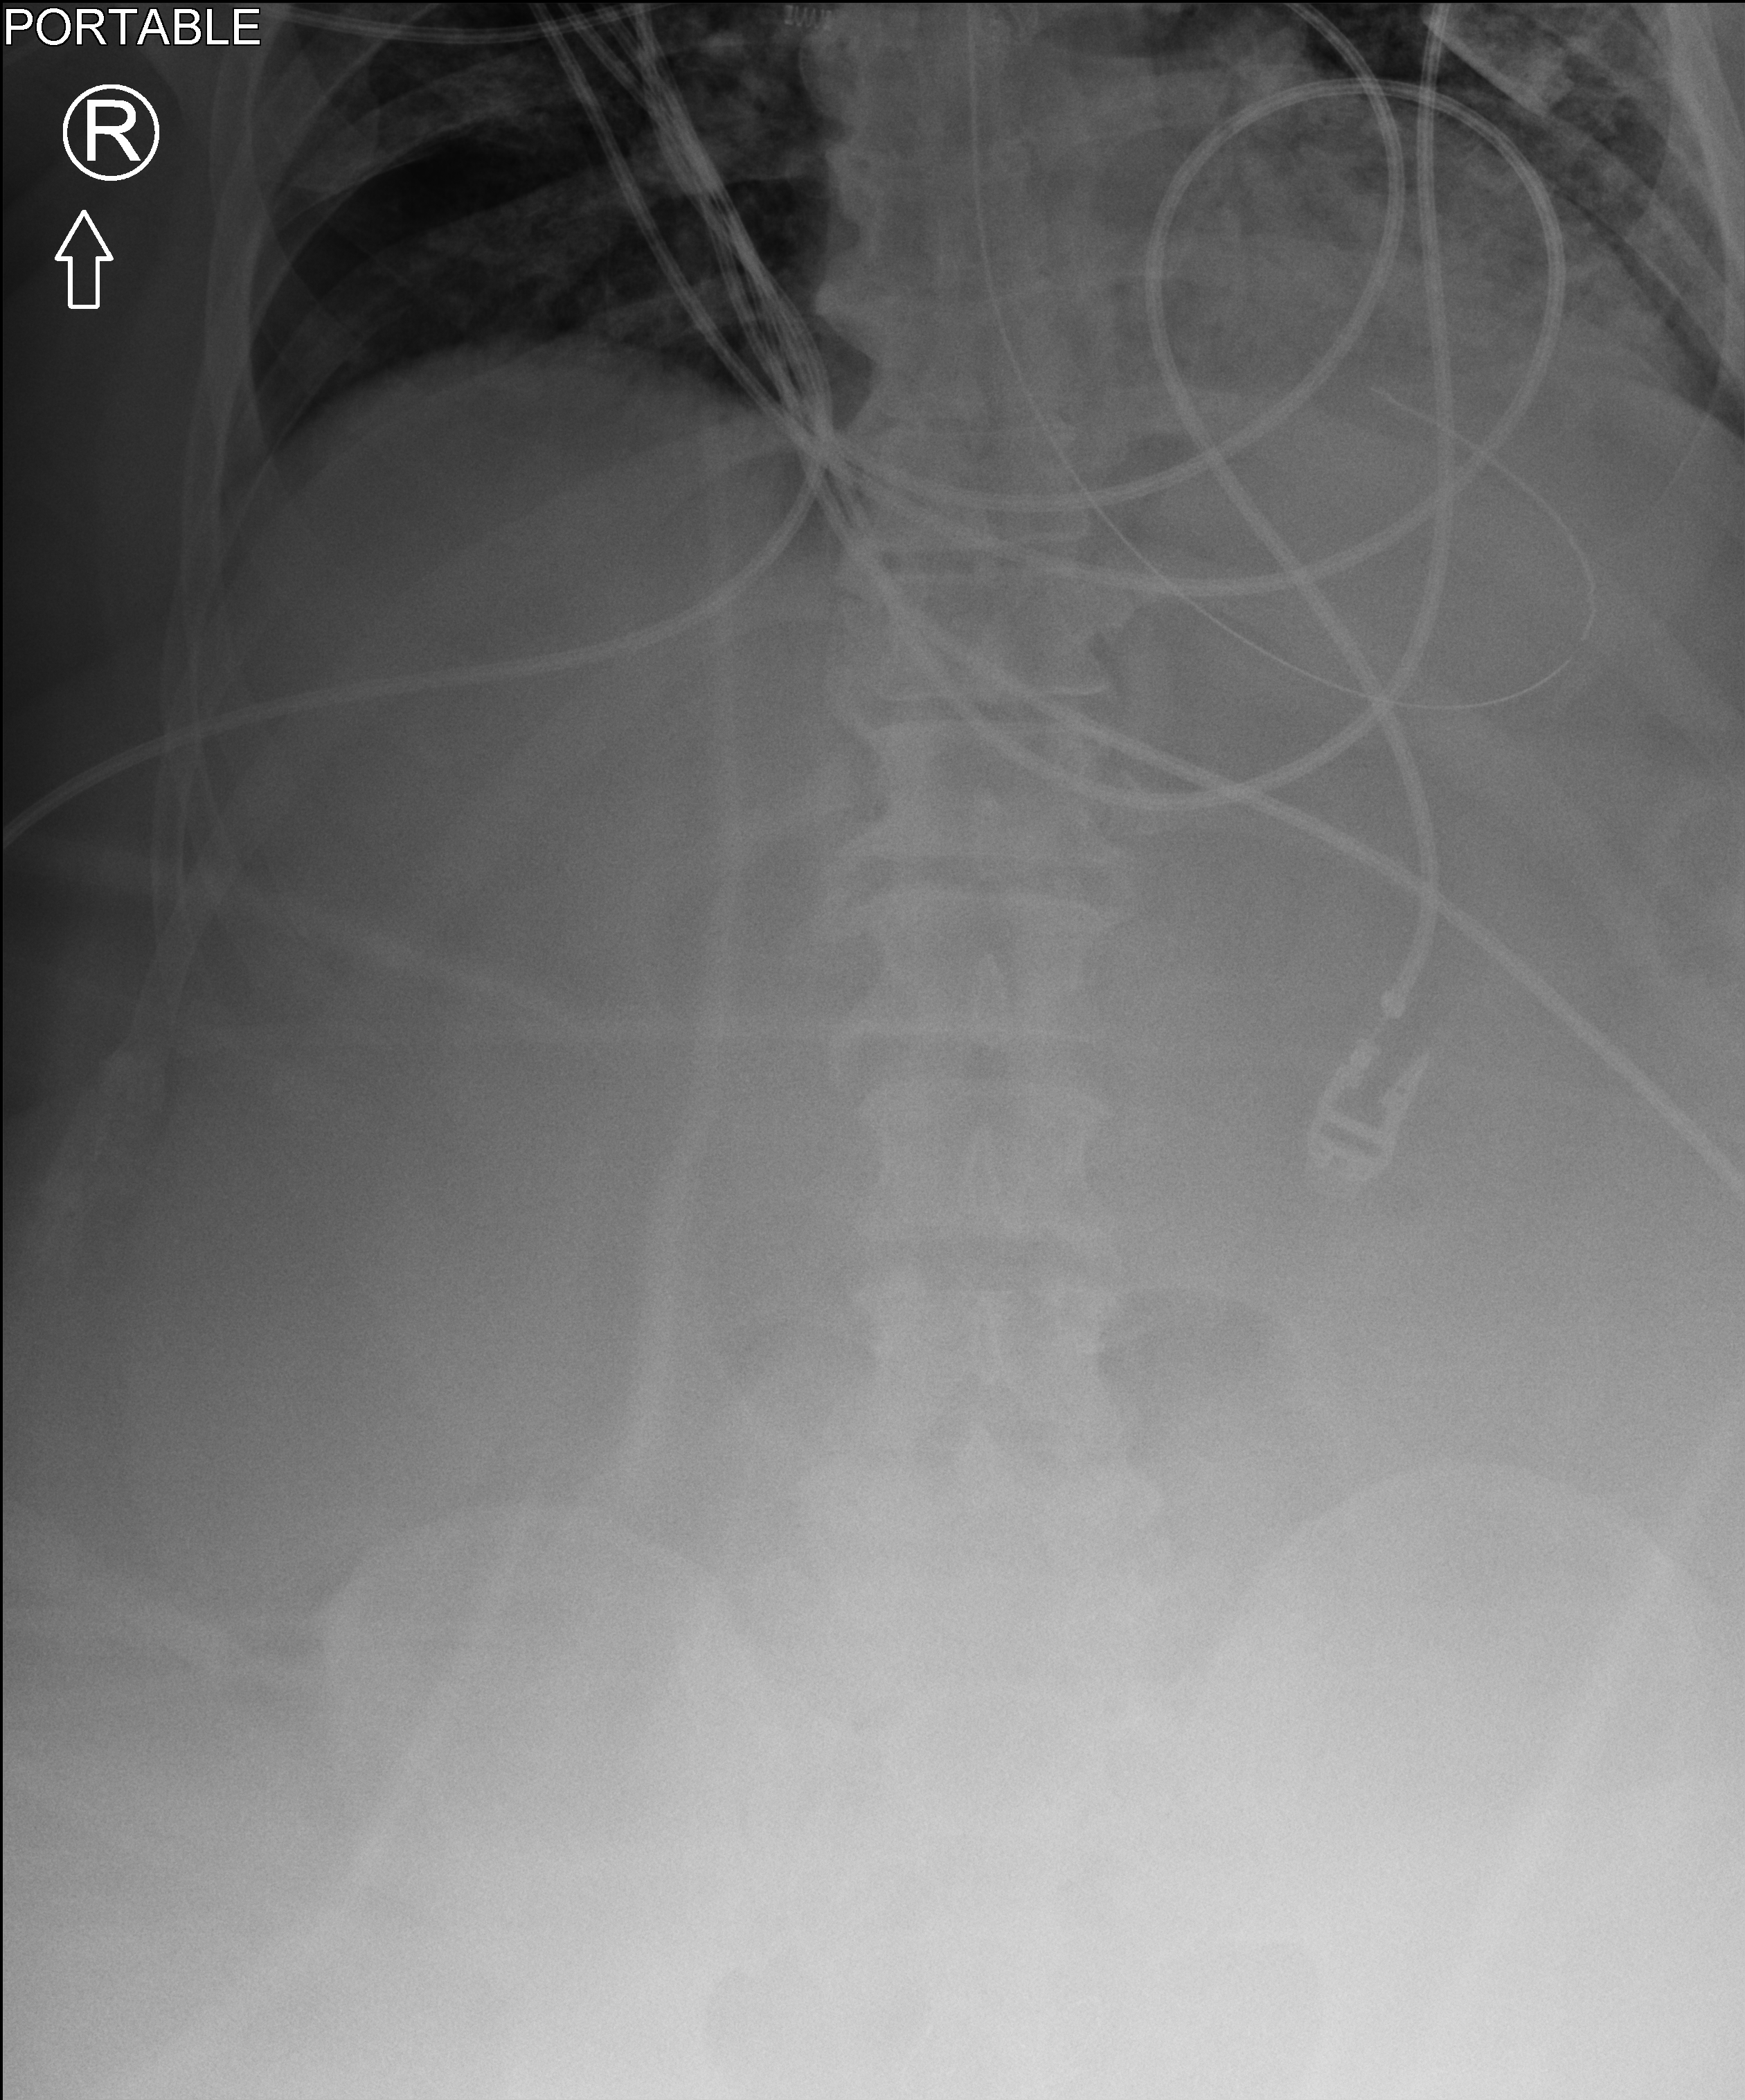
Abdomen X-ray (portable). Adult patient hospitalised with COVID-19, age 18–59 years.
From the hospital-stay record, not from the radiograph (when in the stay this image was taken is not recorded): mechanically ventilated during this hospital stay: yes.